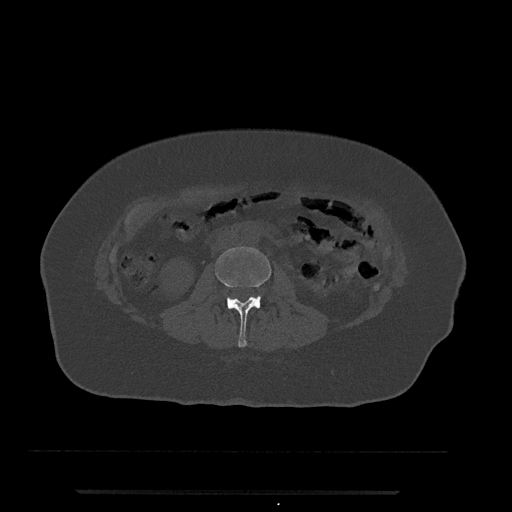
CT including the spine, one axial slice. Slice 23 of 797 in the series (ordered by position). Reconstruction kernel Br40s/3. Bone window (W 1800 / L 400 HU). 0.5 mm slice thickness. 512 × 512 image matrix, field of view 440 × 440 mm. Female patient, age 51 years. From the clinical record (not read from this slice): primary cancer: neuro; vertebrae with lytic lesions (as recorded): T8.
Annotated regions visible in this slice (semi-automatically segmented with operator editing):
- L2 vertebra: bounding box (x1, y1, x2, y2) in pixels: (215, 247, 271, 347)